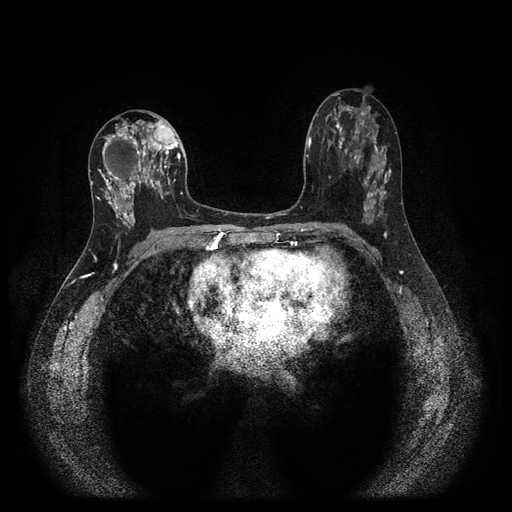
Breast MRI (dynamic contrast-enhanced, multi-phase), one axial slice. Dynamic contrast-enhanced series, time point 2 of 5 at this slice position (early post-contrast). 1.5 T. TE 2.7 ms, TR 5.4 ms. 2 mm slice thickness. 512 × 512 image matrix. Female patient, age 47 years.
Outlined on this slice (semi-automatically segmented with operator editing):
- breast lesion (labelled 'tumour' in the annotation; benign lesions carry a separate 'benign' label): bounding box (x1, y1, x2, y2) in pixels: (95, 118, 179, 230)